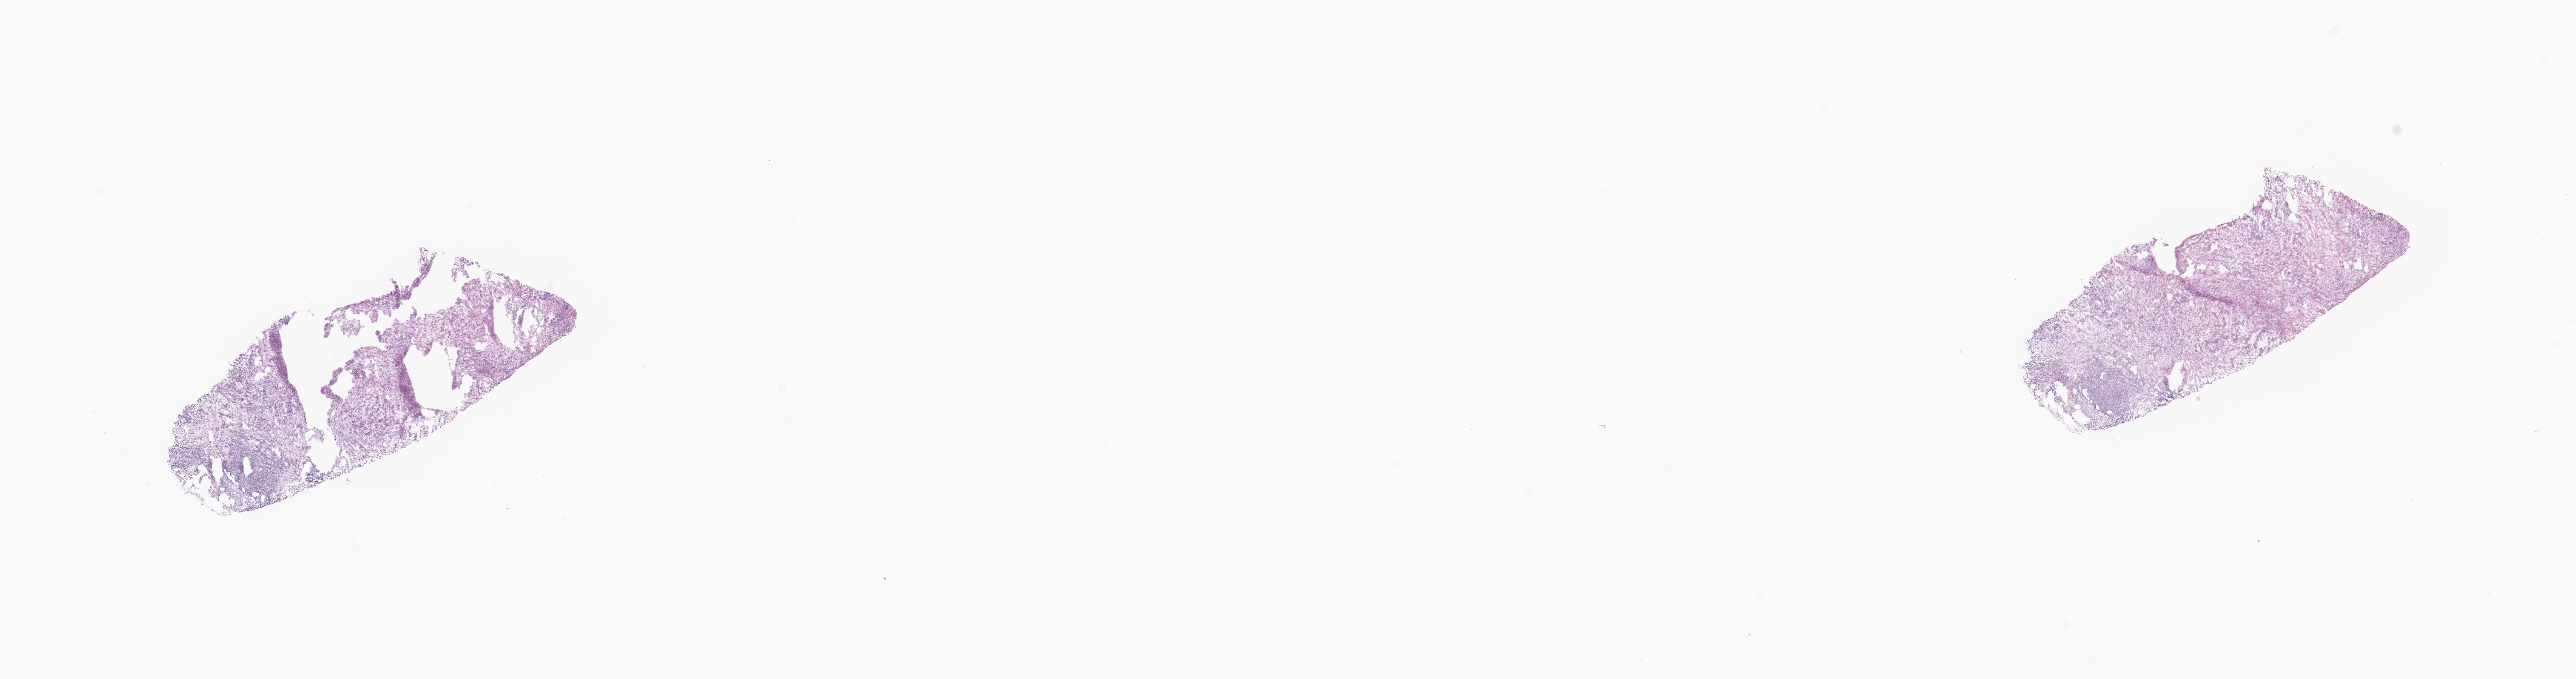
Whole-slide image, H&E stain — shown as a low-resolution overview of the whole scanned area (about 28.8 x 7.6 mm). Frozen section. Specimen: metastatic tumor tissue. Patient: female, age at initial diagnosis 78 years. Slide review estimates, as recorded: tumor cells 70%, tumor nuclei 78%, stromal cells 15%, necrosis 5%, normal cells 10%. Inflammatory infiltration, as recorded: lymphocyte infiltration 12%, monocyte infiltration 0%, neutrophil infiltration 0%.
- patient diagnosis (primary): Infiltrating duct carcinoma, NOS